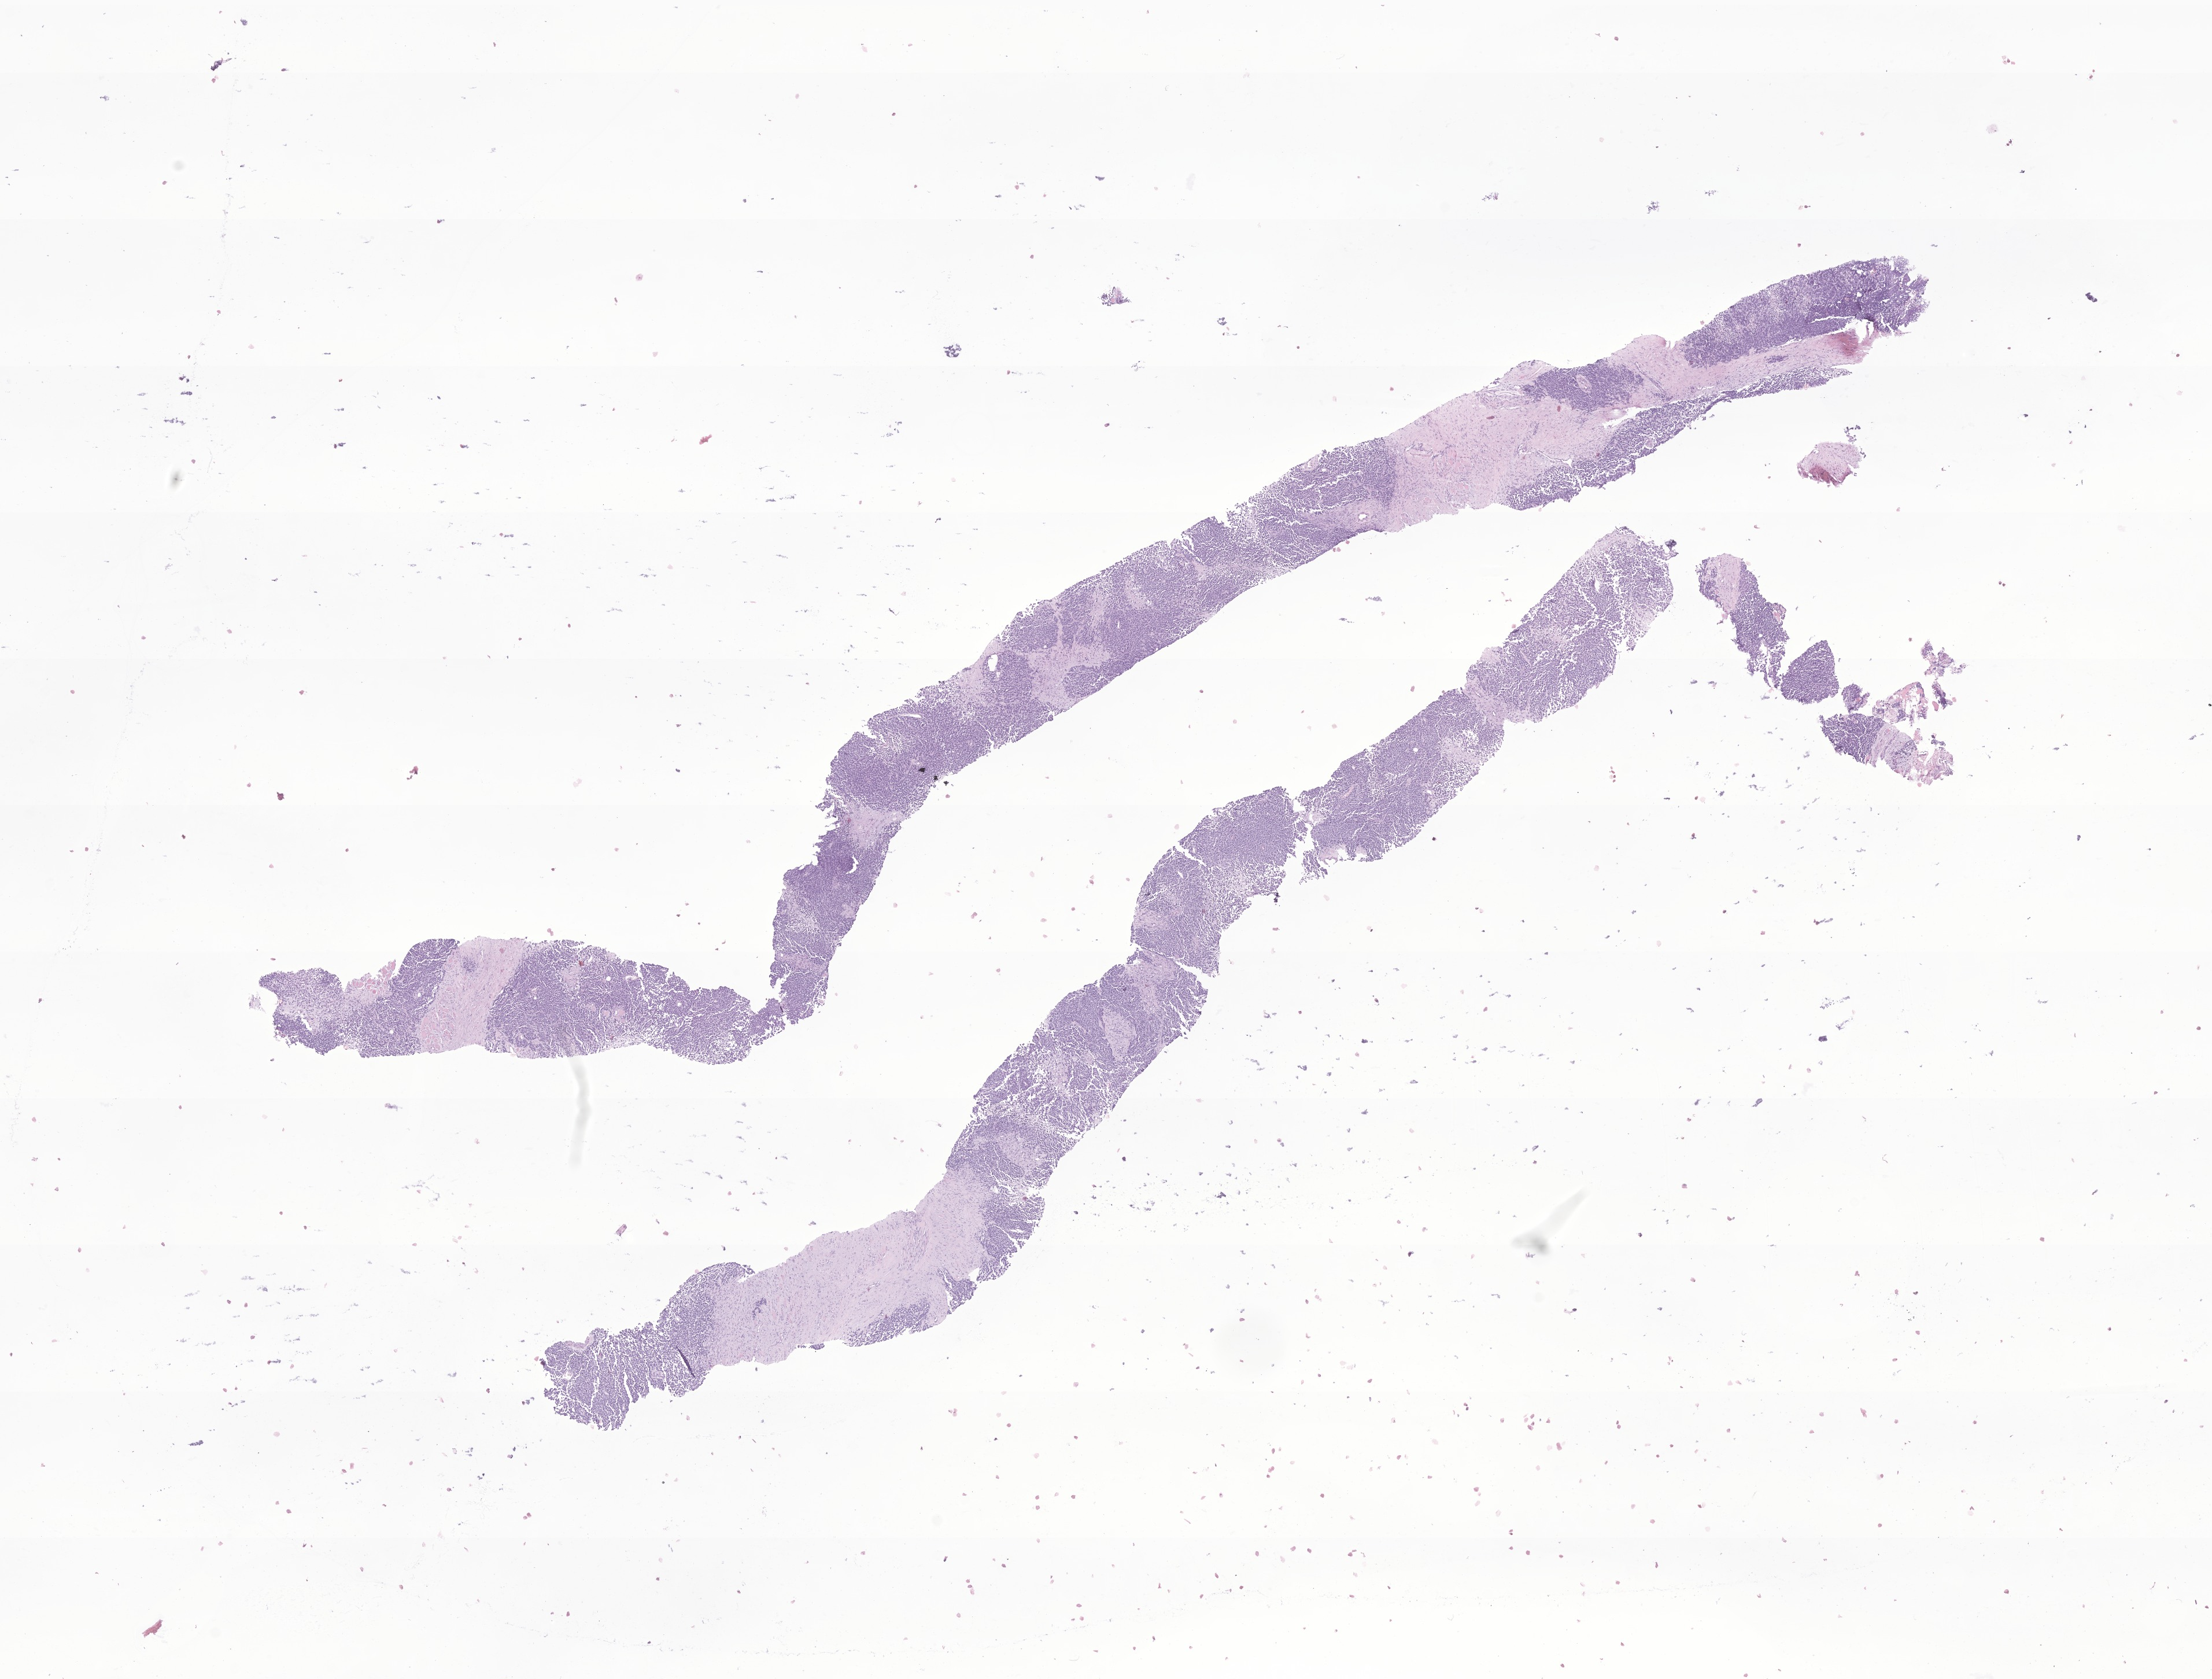
Digitized H&E-stained section of tumor tissue from the prostate — low-resolution overview of the scanned area, about 16.1 x 12.2 mm; formalin-fixed, paraffin-embedded (FFPE) tissue. Patient: male, age 162 months (13 years 6 months).
Recorded diagnosis: Alveolar rhabdomyosarcoma.